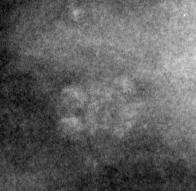
Region of interest cut from a scanned film mammogram (one marked finding); left breast; MLO view.
- Marked abnormality: calcifications, morphology amorphous, distribution clustered; BI-RADS assessment category 4; pathology result (as recorded, not read from the image): malignant.